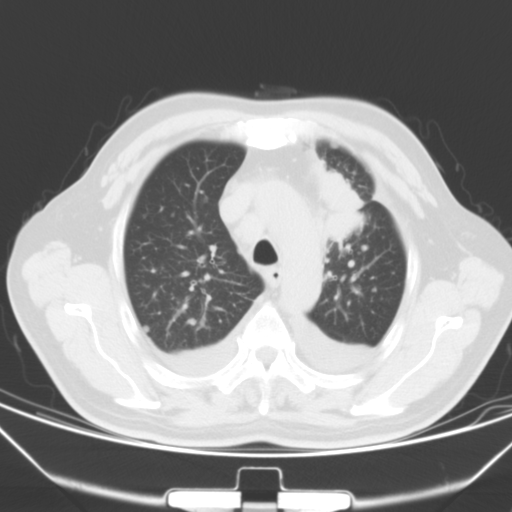
Chest CT, one axial slice; slice 48 of 66 in the series (ordered by position); 120 kVp; lung window (W 1500 / L -600 HU); 5 mm slice thickness; 512 × 512 image matrix. Patient: male, 66 years. Case-level facts recorded for this patient, not image findings: clinical TNM (as recorded): T1c N0 M0.
Structures marked on this image (rectangle marked by the reading radiologist):
- lung tumour (recorded histology: adenocarcinoma): bounding box [x1, y1, x2, y2] px = [313, 159, 366, 248]